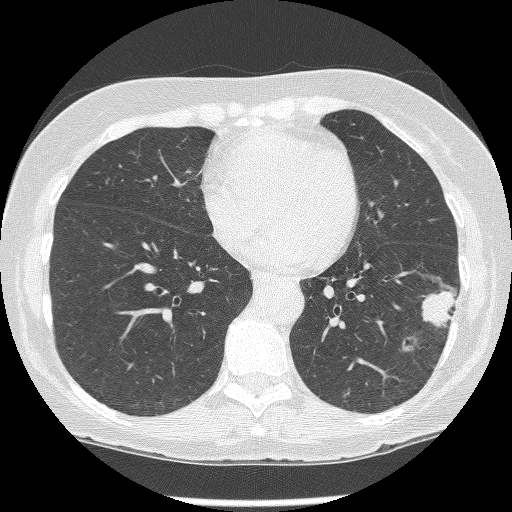
Low-dose screening chest CT, axial slice, baseline annual screen, lung window (W 1500 / L -600 HU), lung (sharp) reconstruction kernel (BONE), slice 96 of 247 in the series, 512 × 512 image matrix. Female, age 62 years at enrolment. Former smoker at enrolment.
Expert-annotated lung lesion, bounding box (x1, y1, x2, y2) in pixels: (416, 283, 461, 339). The screening reader recorded 2 non-calcified nodules or masses ≥4 mm on this exam (left lower lobe, left lower lobe); which of them this box marks is not recorded. Later outcome: lung cancer diagnosed 15 days after this screen — non-small cell carcinoma, left lower lobe, stage IIIB (AJCC 6th edition), 23 mm at pathology.